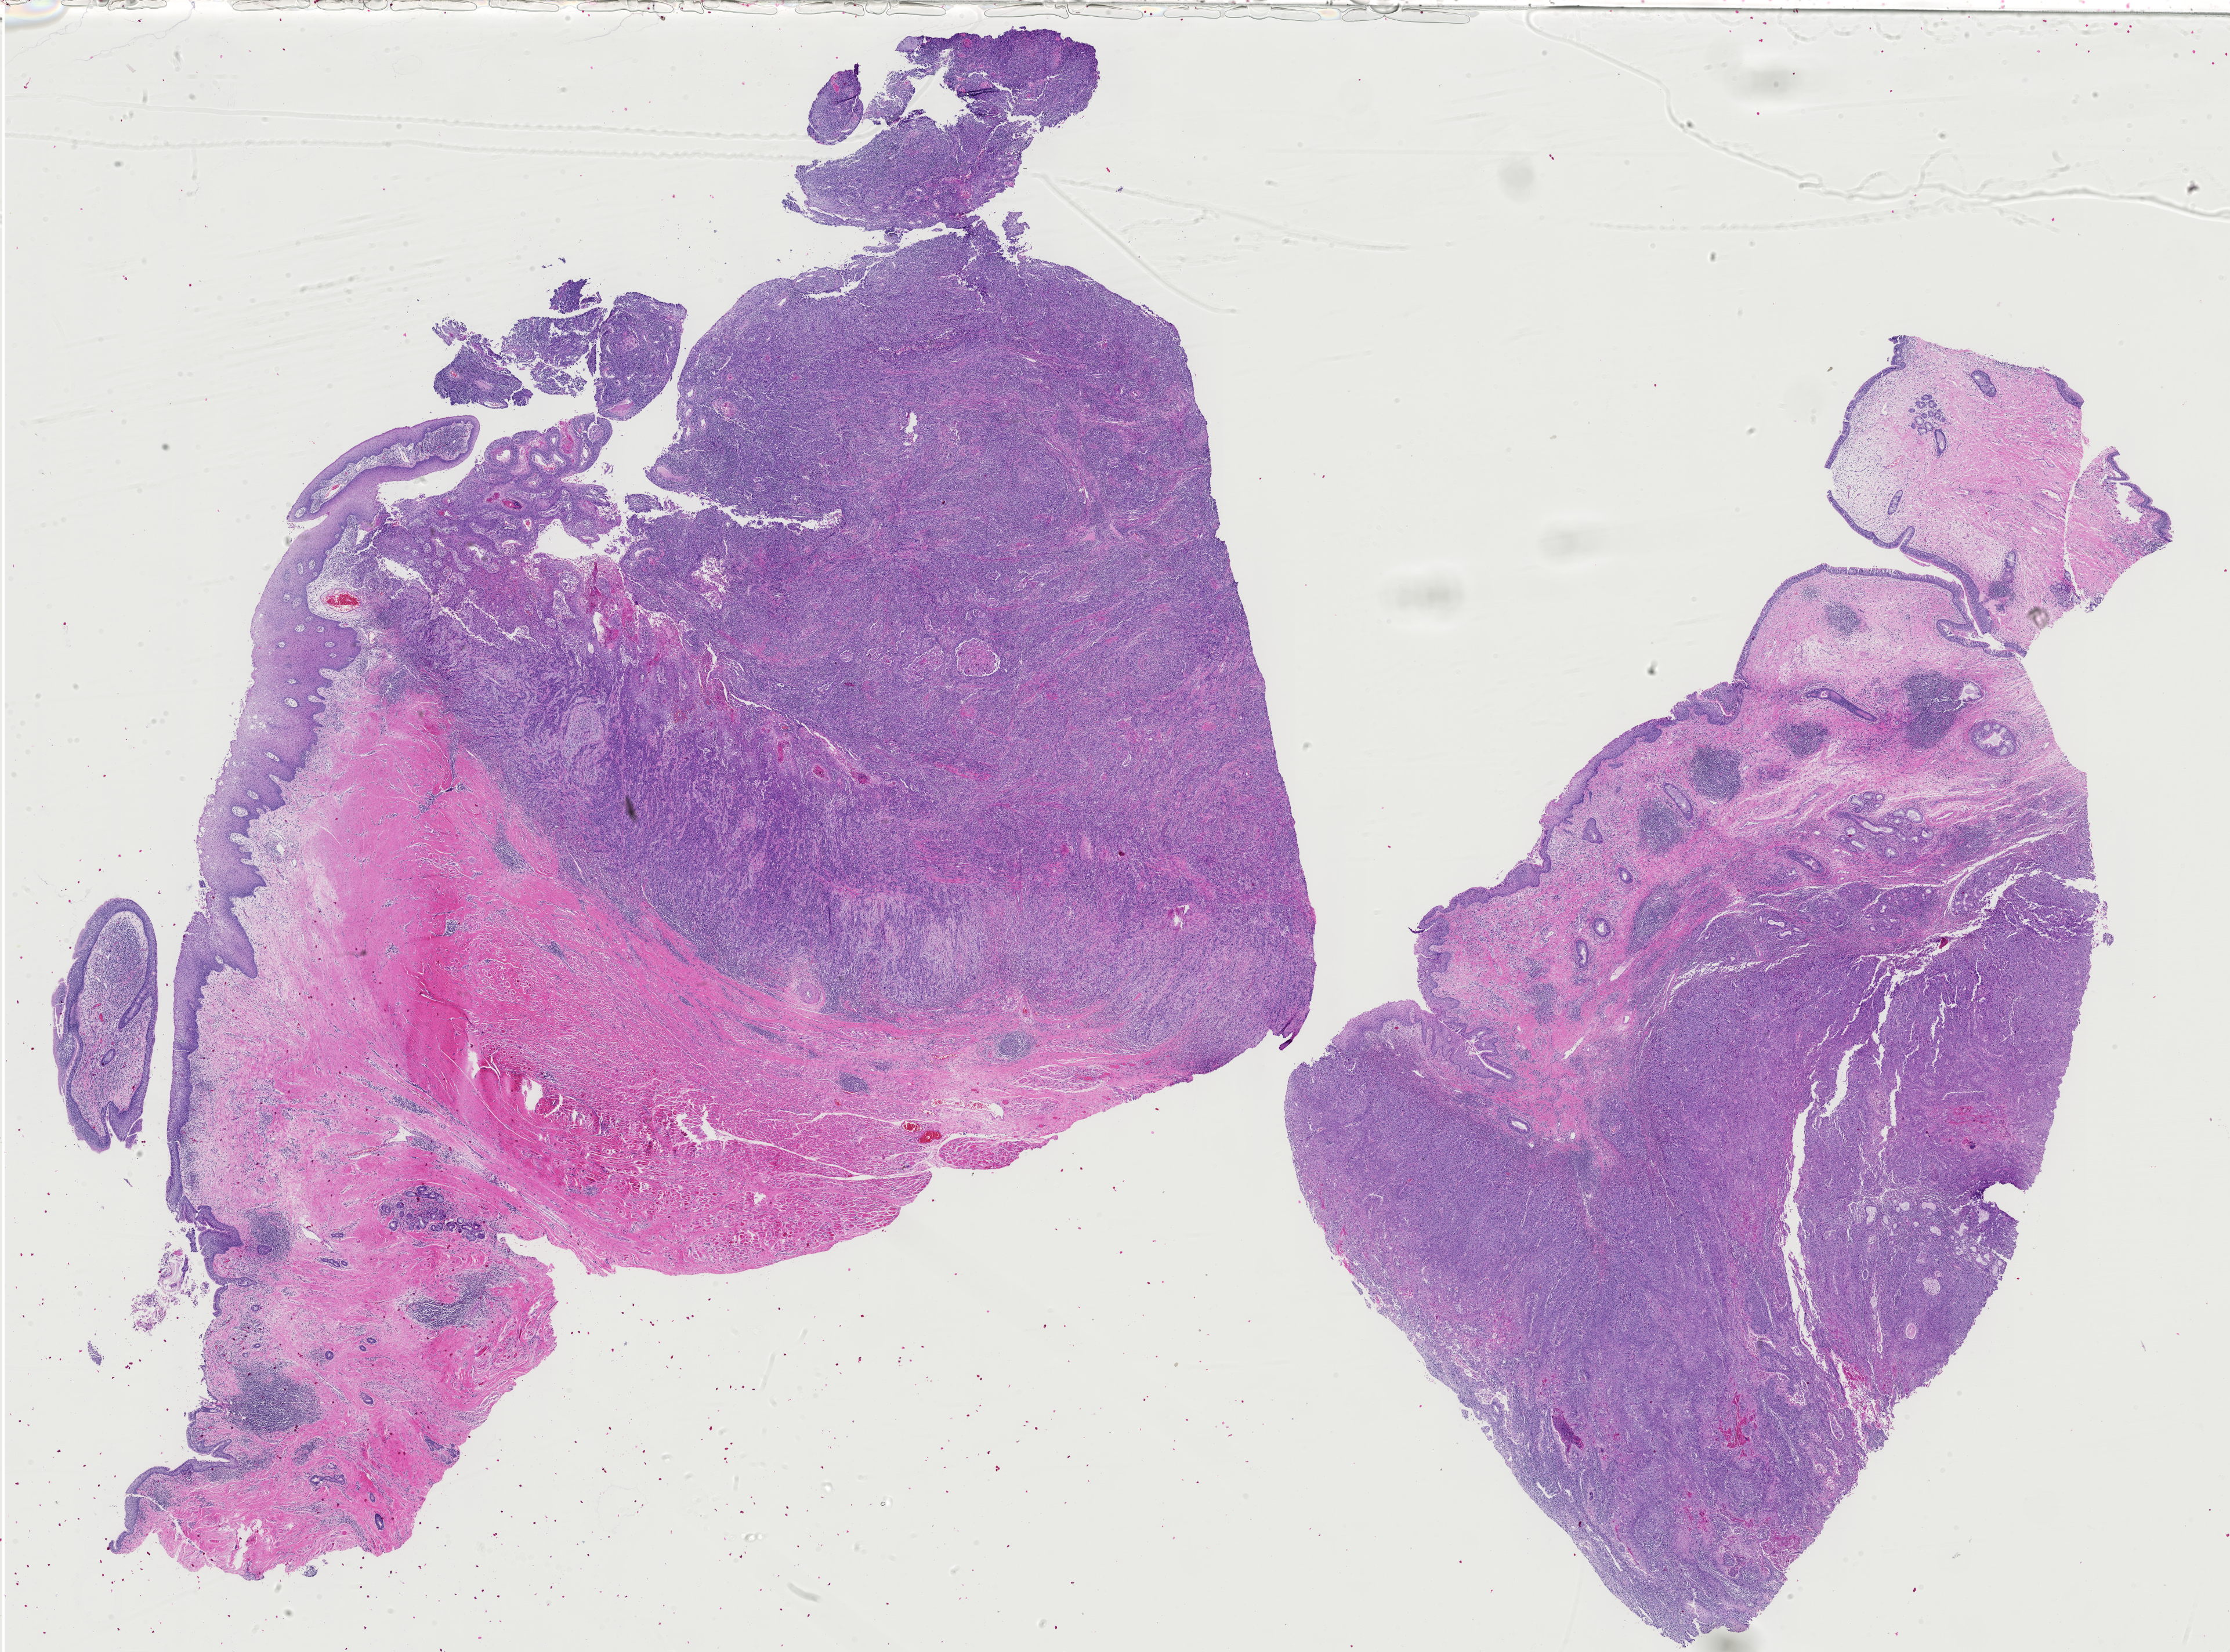
Whole-slide histology image, H&E — whole scanned area (about 27.9 x 20.7 mm, slide scanned at 40x) shown as a low-resolution overview; FFPE section; sample: primary tumour, head and neck. Patient: female, age at initial diagnosis 79 years. Histologic grade: G1 (well differentiated).
* AJCC pathologic stage: IVA (7th edition)
* TNM: T4 NX MX
* pathologic diagnosis: Squamous cell carcinoma, NOS